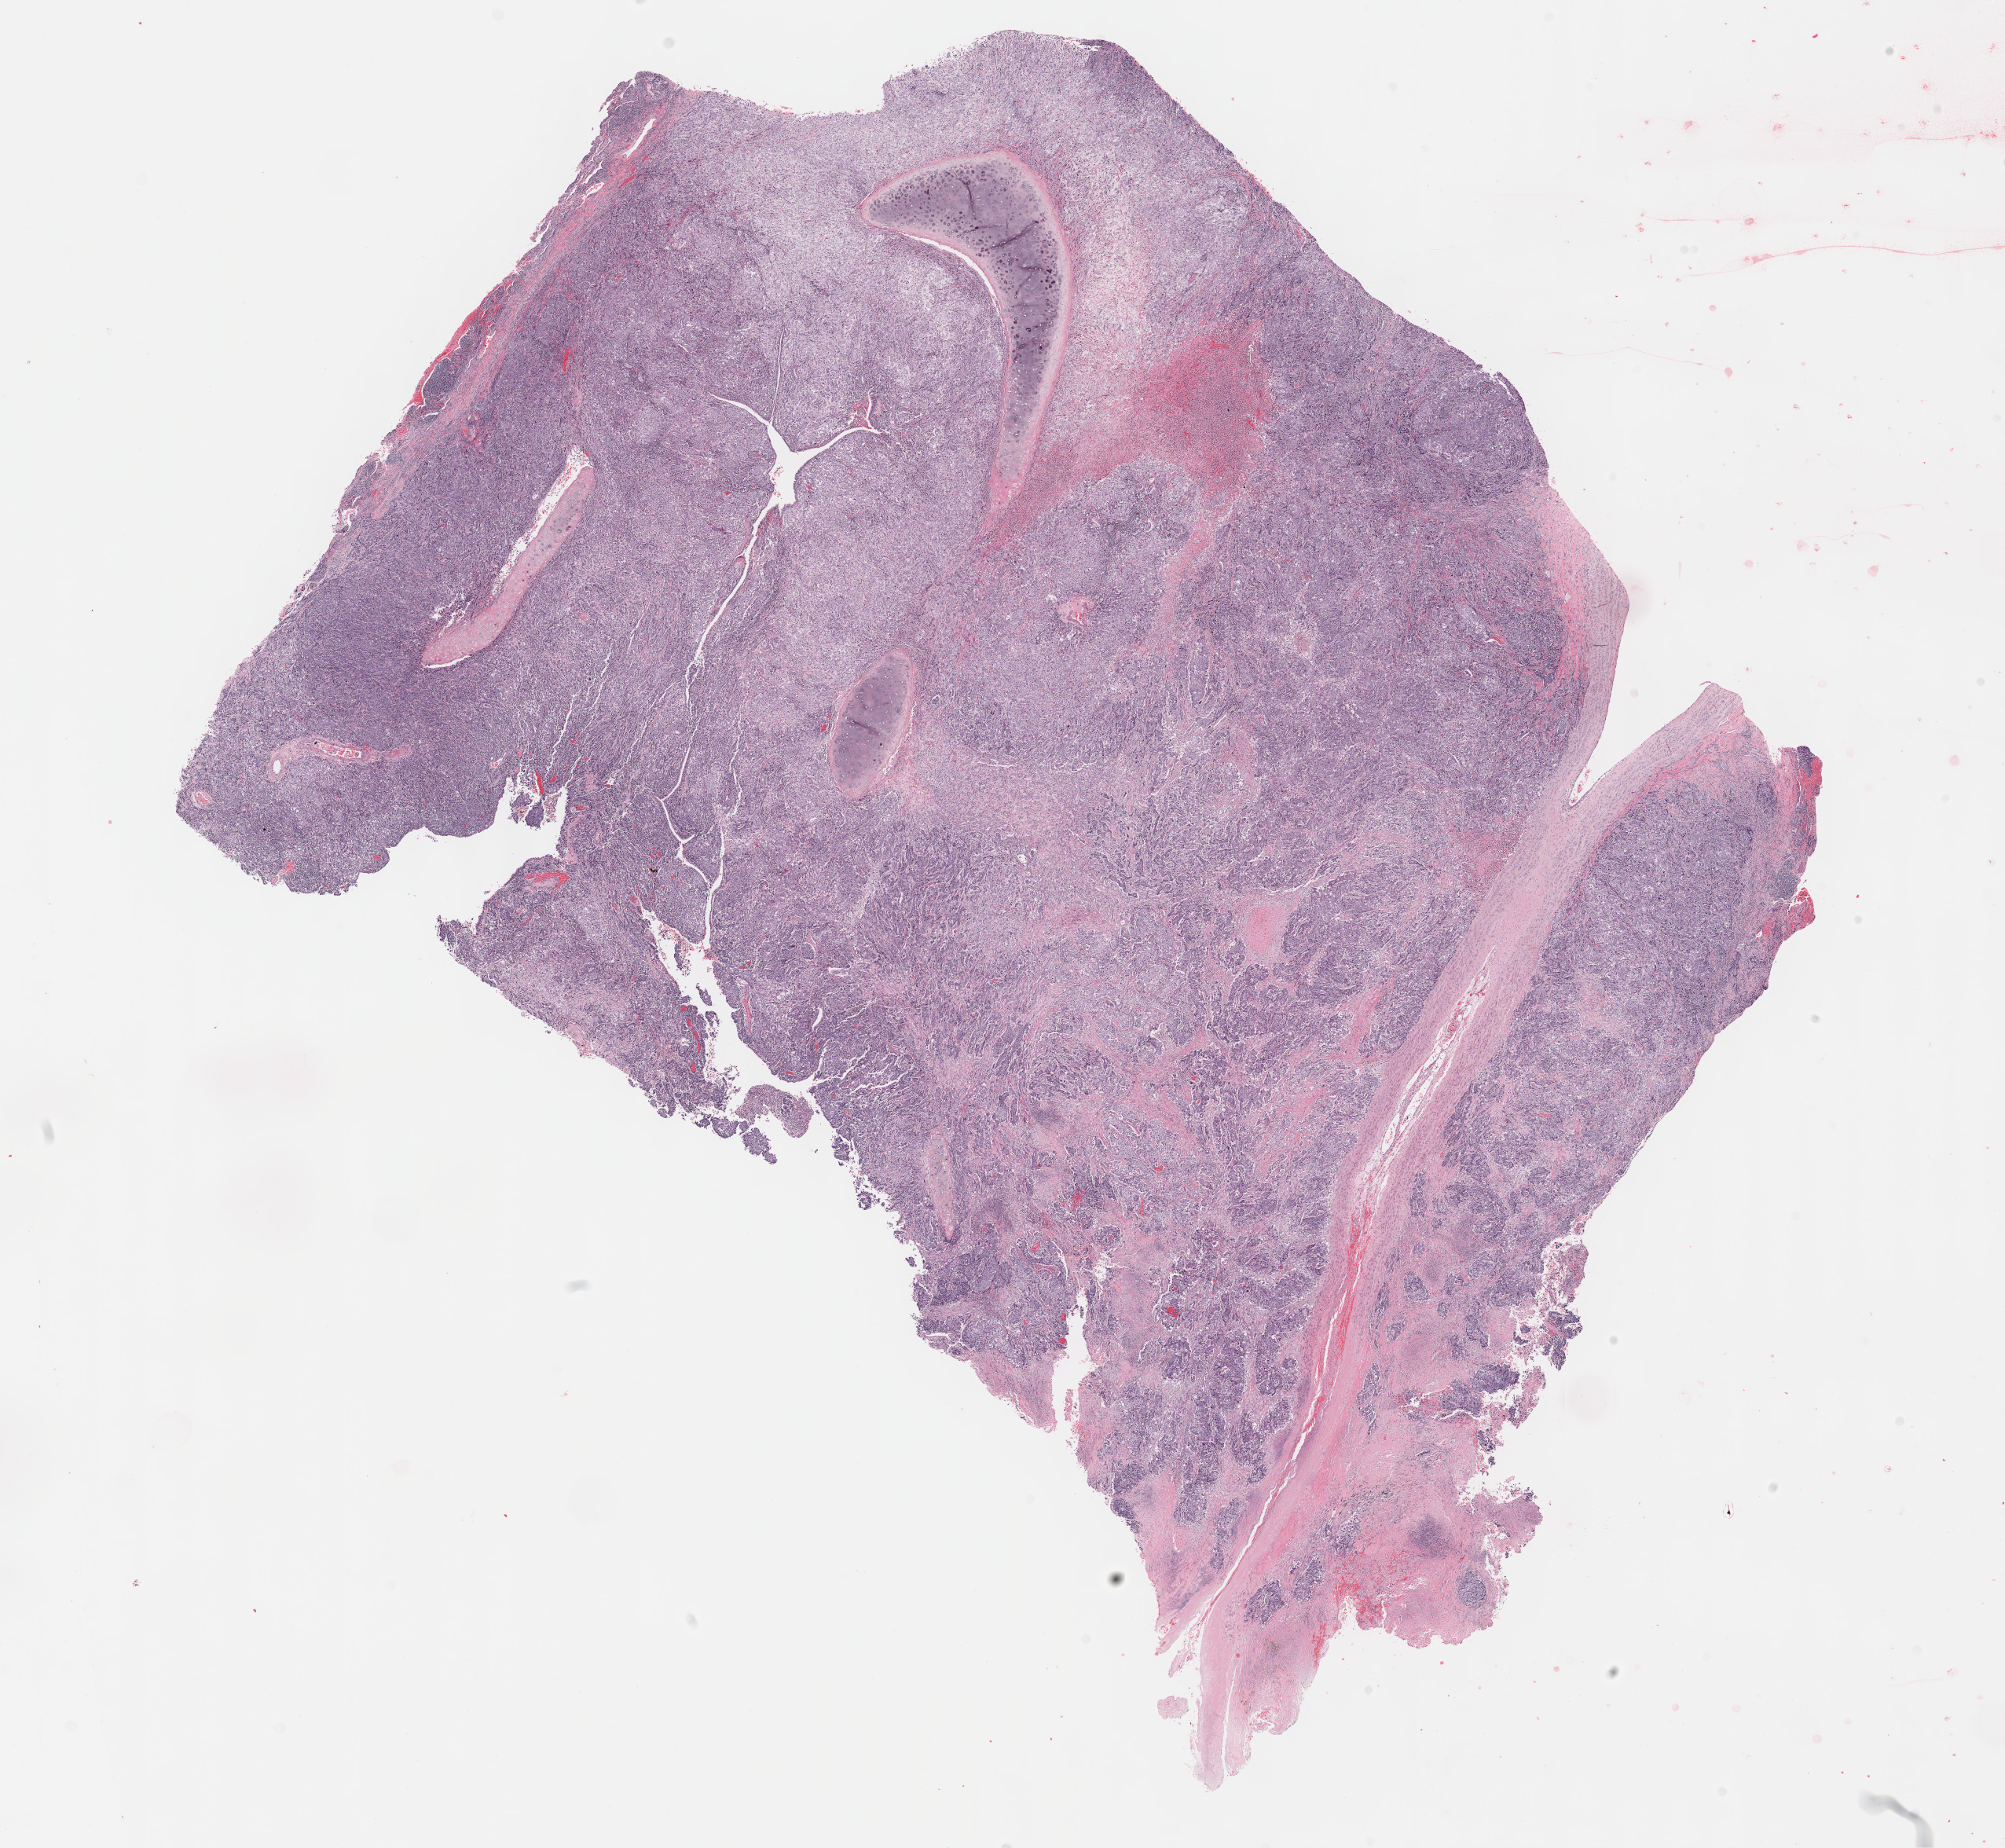
H&E-stained whole-slide image — a low-resolution overview of the entire scanned area, about 20.6 x 19.0 mm. Formalin-fixed paraffin-embedded (FFPE) diagnostic section. Primary tumour sample from the lung. Male, age 65 years at initial diagnosis.
- laterality: left
- AJCC pathologic stage: IIIA
- diagnosis: Squamous cell carcinoma, NOS (upper lobe, lung)